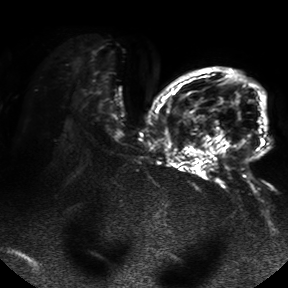
Breast MRI, one axial slice; slice 27 of 50 in the series (ordered by position); diffusion-weighted series; image 2 of 4 stored at this slice position (different b-values; order by instance number); 1.5 T; 4 mm slice thickness; 288 × 288 image matrix, field of view 390 × 390 mm. Female patient.
Outlined on this slice (expert manual segmentation):
- tumour on diffusion-weighted imaging: bounding box [x1, y1, x2, y2] px = [174, 94, 240, 116]